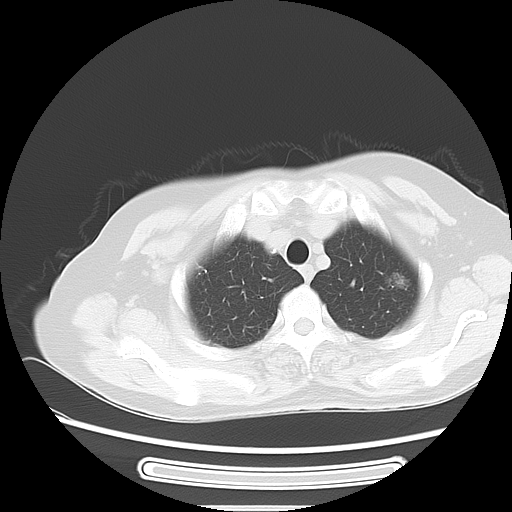
Chest CT, one axial slice. 120 kVp. Lung window (W 1500 / L -600 HU). 512 × 512 image matrix, field of view 350 × 350 mm. Patient: female, 57 years. From the clinical record (not read from this slice): clinical TNM (as recorded): T1c N0 M0; histopathological grade: G2-3.
Annotated regions visible in this slice (bounding box drawn by a radiologist):
- lung tumour (recorded histology: adenocarcinoma): bounding box <383,265,410,291> (left, top, right, bottom; pixels)